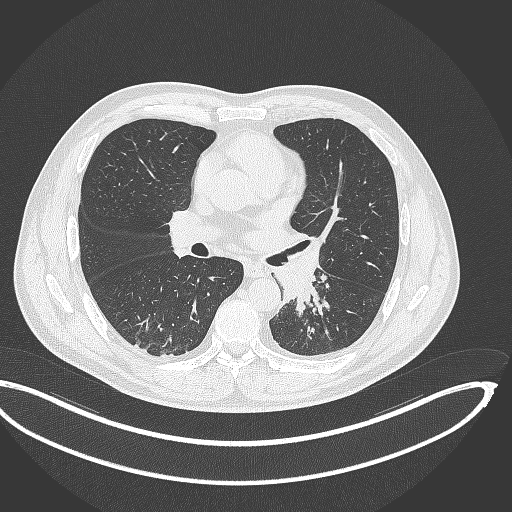
Chest CT, one axial slice. Slice 194 of 362 in the series (ordered by position). Lung window (W 1500 / L -600 HU). 1 mm slice thickness. 512 × 512 image matrix, field of view 442 × 442 mm. Patient: male, 50 years. From the clinical record (not read from this slice): clinical TNM (as recorded): T2a N3 M0.
Outlined on this slice (bounding box drawn by a radiologist):
- lung tumour (recorded histology: squamous cell carcinoma): box from (x=279, y=268) to (x=326, y=314) px